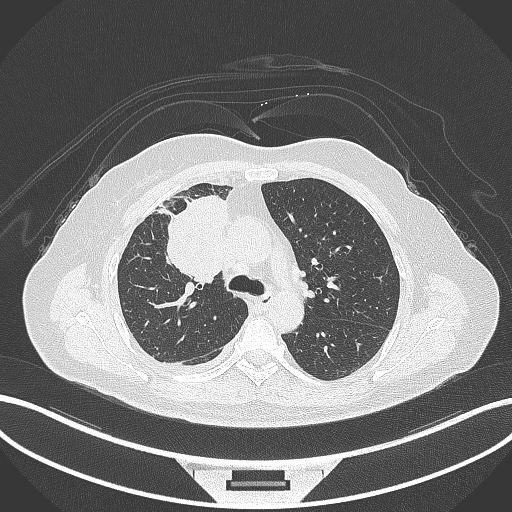
Chest CT, one axial slice. Slice 189 of 305 in the series (ordered by position). Reconstruction kernel B70f. Lung window (W 1500 / L -600 HU). 1 mm slice thickness. 512 × 512 image matrix, field of view 400 × 400 mm. Patient: female, 52 years. From the clinical record (not read from this slice): clinical TNM (as recorded): T3 N1 M1.
Annotated regions visible in this slice (rectangle marked by the reading radiologist):
- lung tumour (recorded histology: adenocarcinoma): bounding box <162,187,229,286> (left, top, right, bottom; pixels)